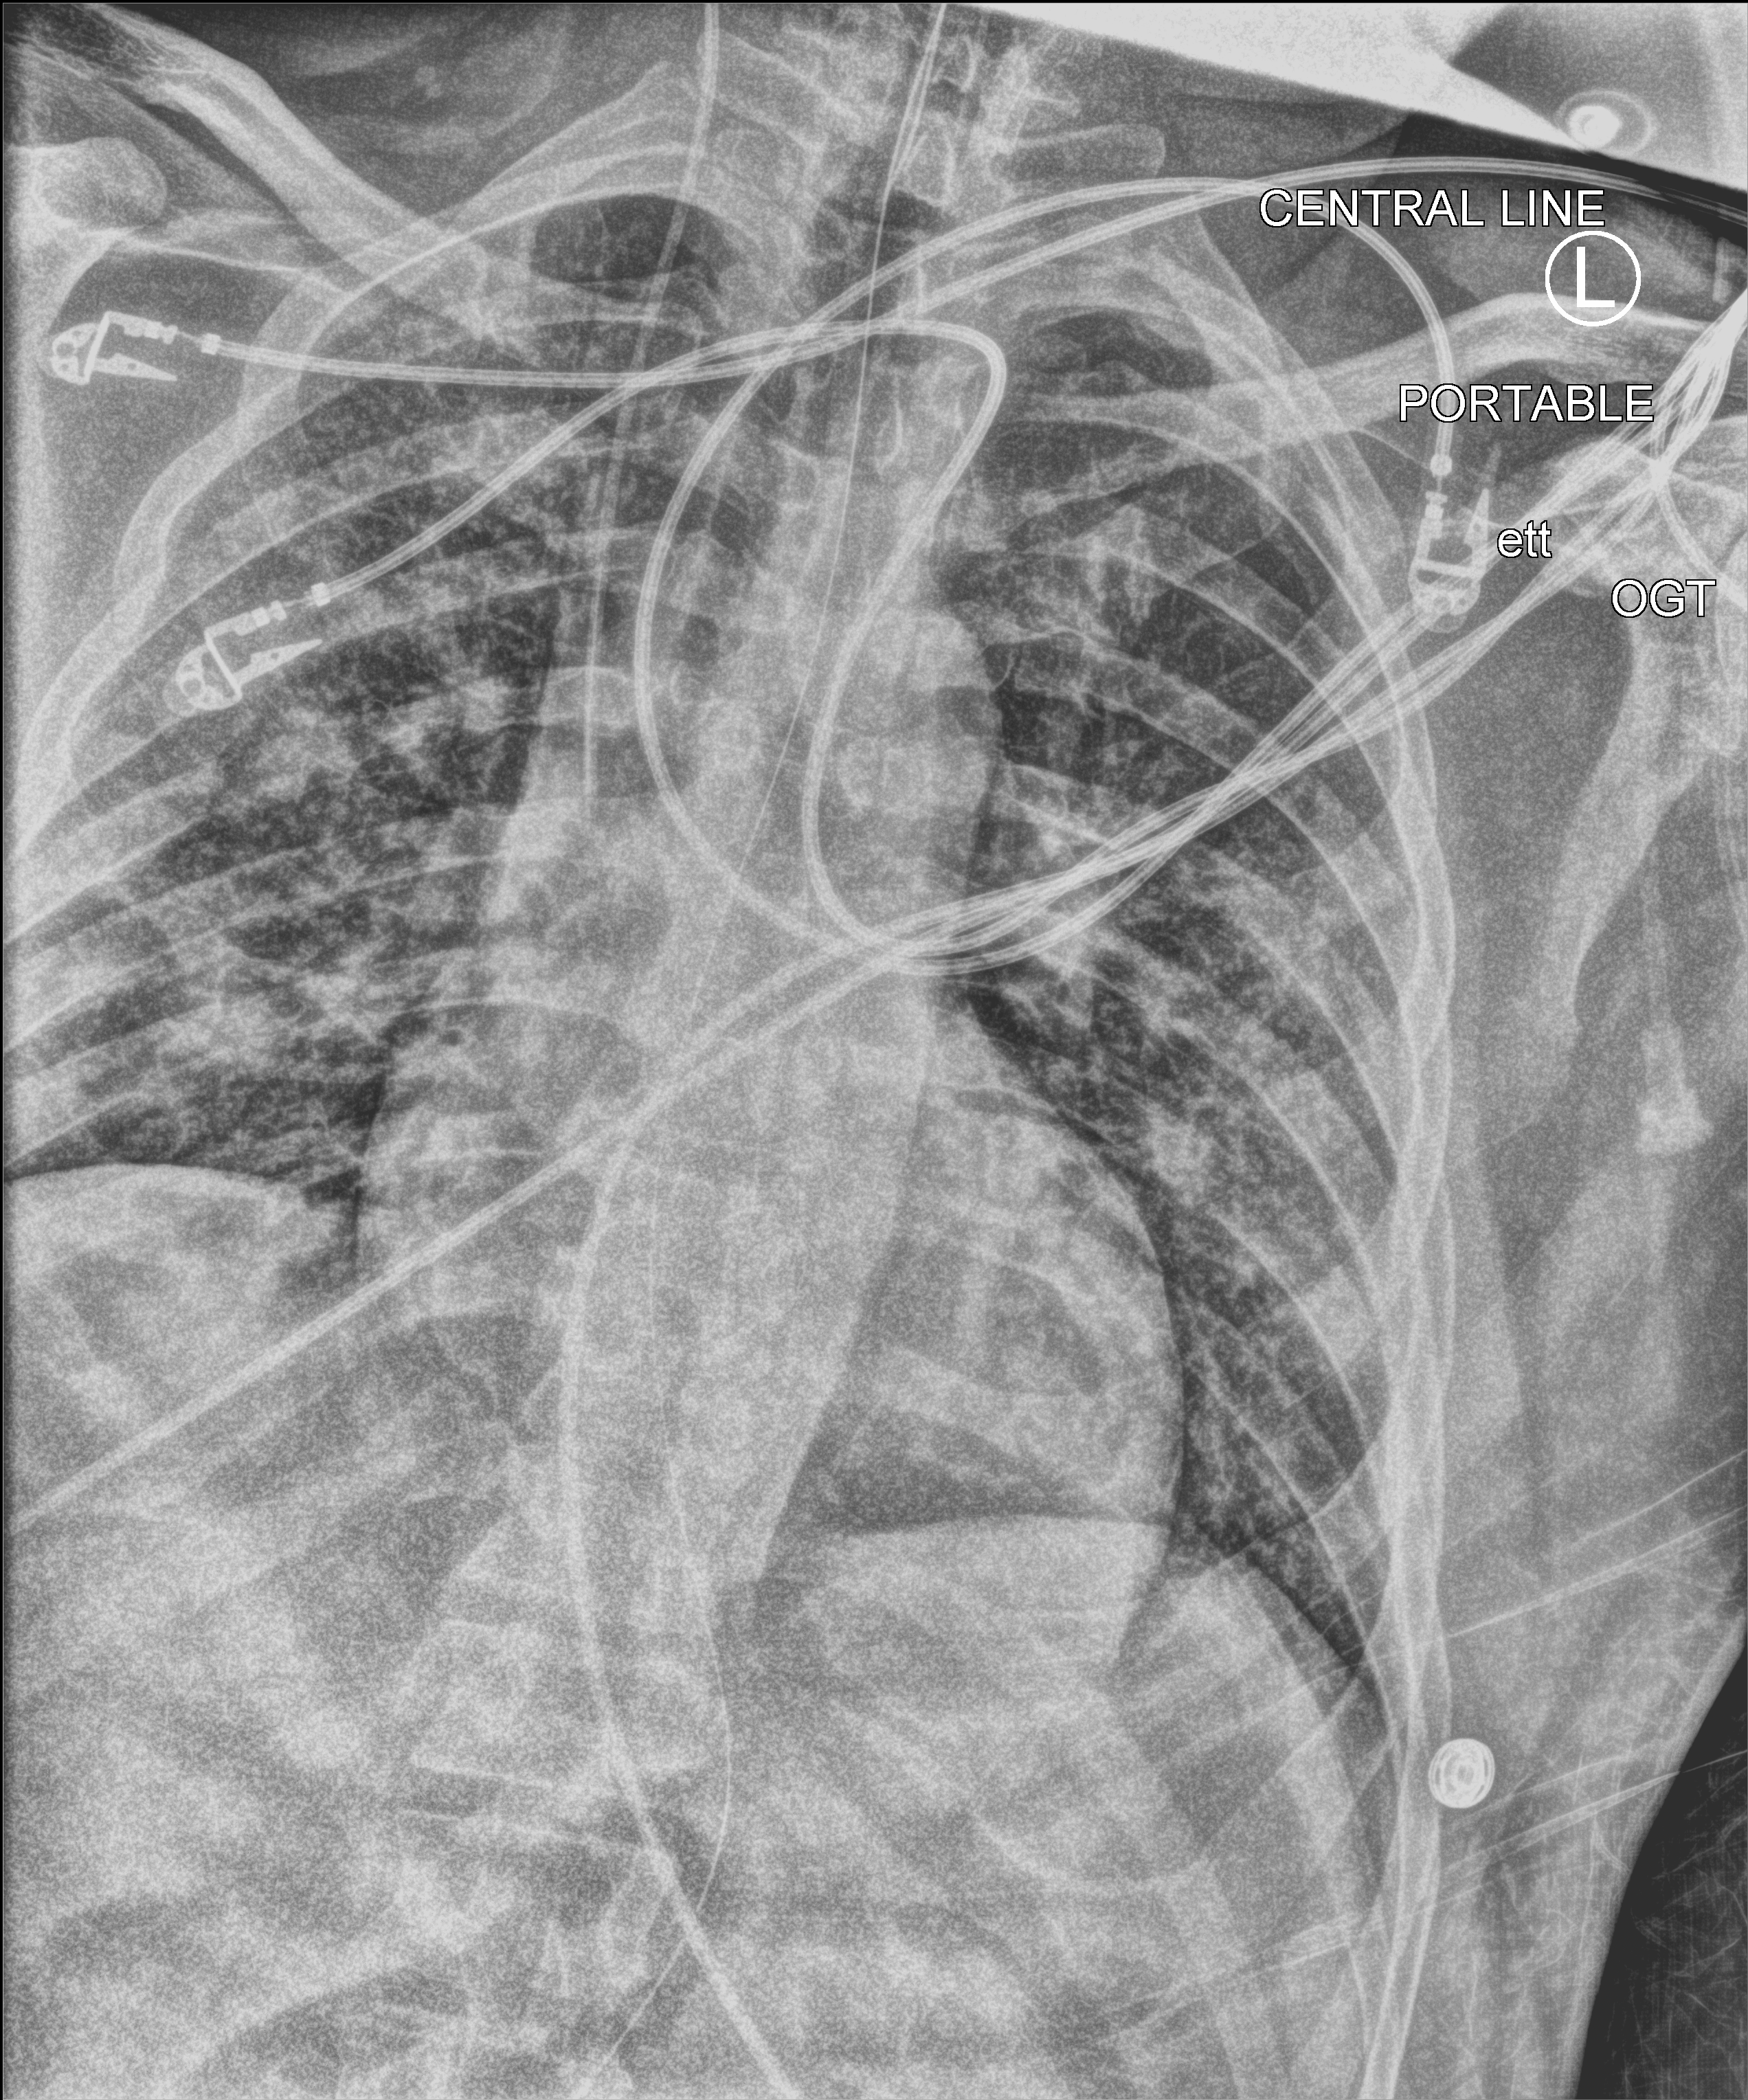
Chest X-ray (portable). Male patient hospitalised with COVID-19, age 18–59 years.
Hospital-stay facts (about this admission, not read from this image; timing relative to this image not recorded): mechanically ventilated during this hospital stay: yes; admitted to intensive care during this hospital stay: no.